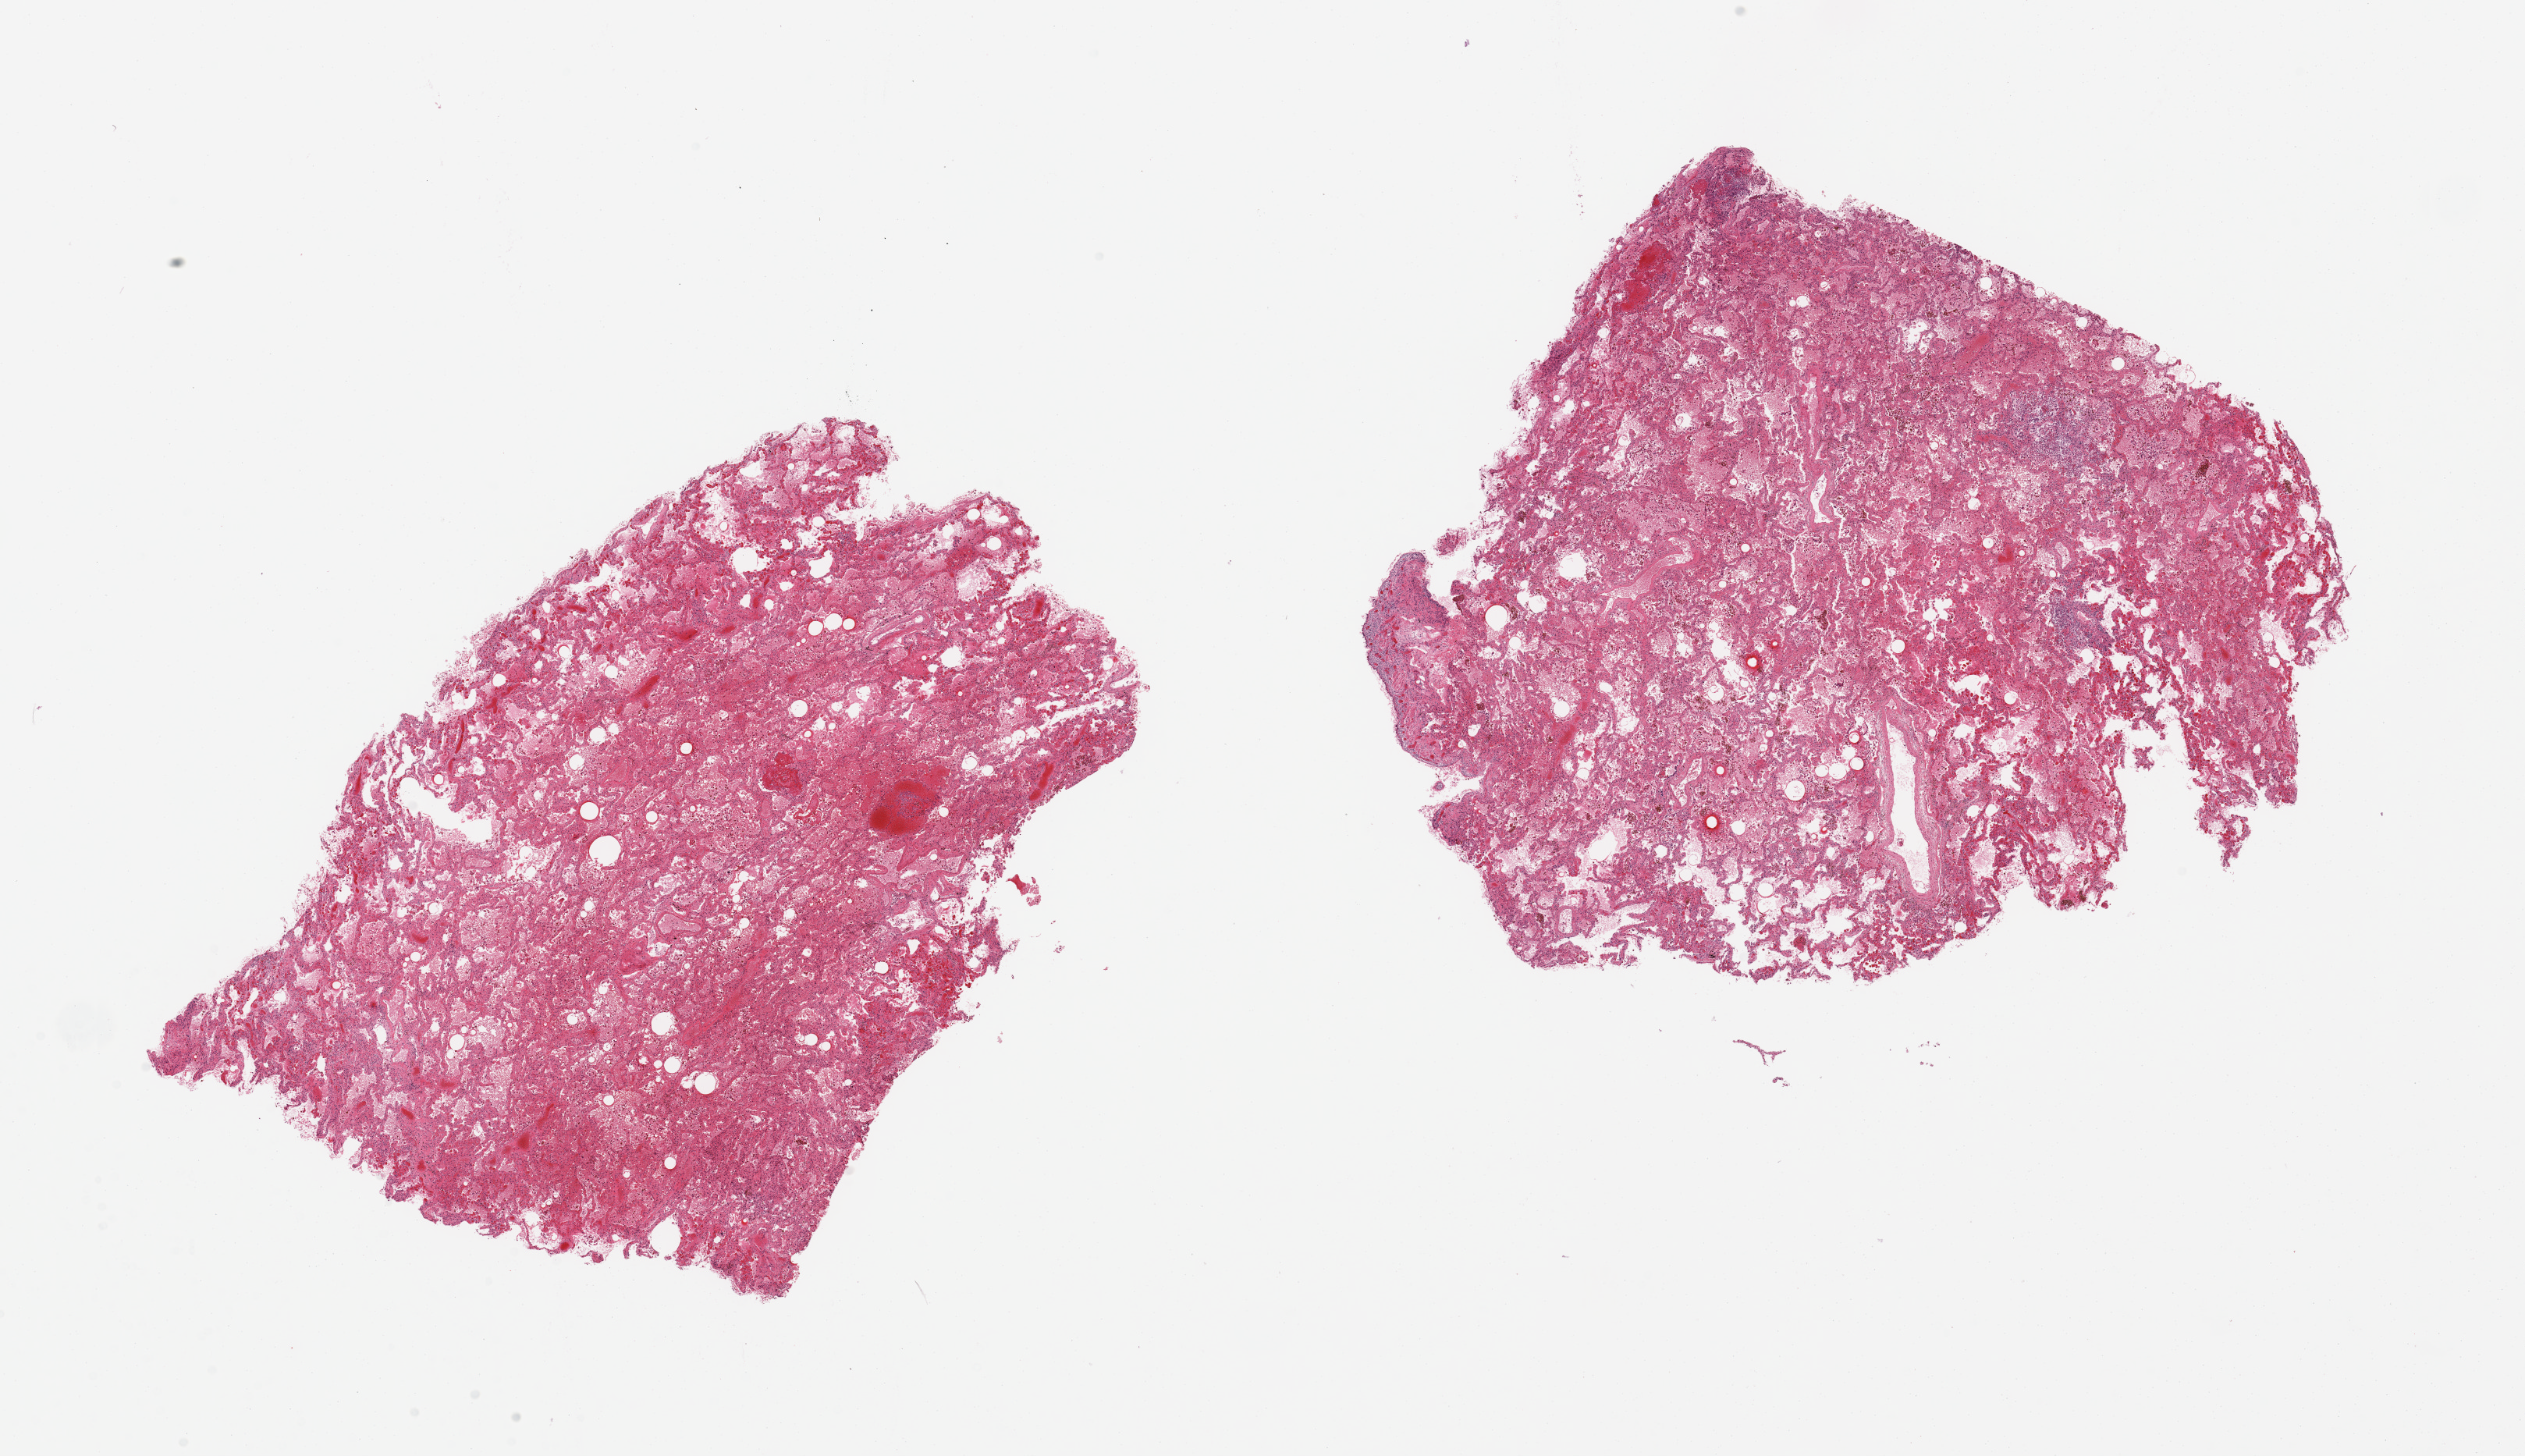
Digitized haematoxylin and eosin-stained section, brightfield, whole scanned area (about 25.6 x 14.8 mm, from a 20x scan) shown as a low-resolution overview; PAXgene-fixed, paraffin-embedded tissue; target tissue: lung; tissue donor sample. Male donor.
• reviewer comment on this tissue sample: 2 pieces; severe congestion; large numbers of alveolar macrophages; patchy edema, hemorrhage and pneumonitis